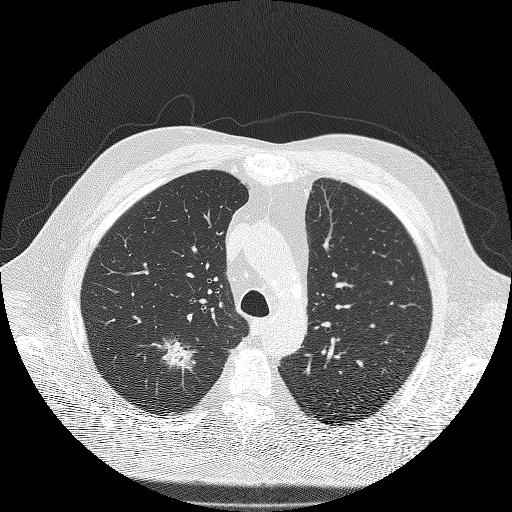
Low-dose screening chest CT, one axial slice. Position 143 of 180 along the scan axis. 120 kVp. Lung window (W 1500 / L -600 HU). 512 × 512 image matrix, field of view 385 × 385 mm.
Annotated regions visible in this slice (manually delineated by an expert):
- lesion 1 (tumor, upper lobe of right lung): bounding box <151,339,197,373> (left, top, right, bottom; pixels)